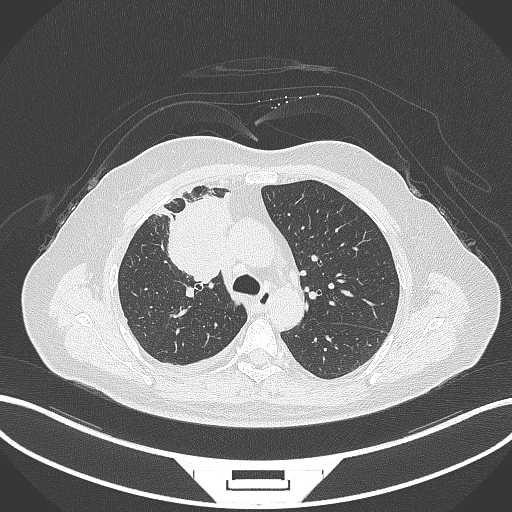
Chest CT, one axial slice; slice 195 of 305 in the series (ordered by position); reconstruction kernel B70f; lung window (W 1500 / L -600 HU); 1 mm slice thickness; 512 × 512 image matrix, field of view 400 × 400 mm. Female patient, age 52 years. From the clinical record (not read from this slice): clinical TNM (as recorded): T3 N1 M1.
Structures marked on this image (bounding box drawn by a radiologist):
- lung tumour (recorded histology: adenocarcinoma): bounding box <154,185,233,295> (left, top, right, bottom; pixels)